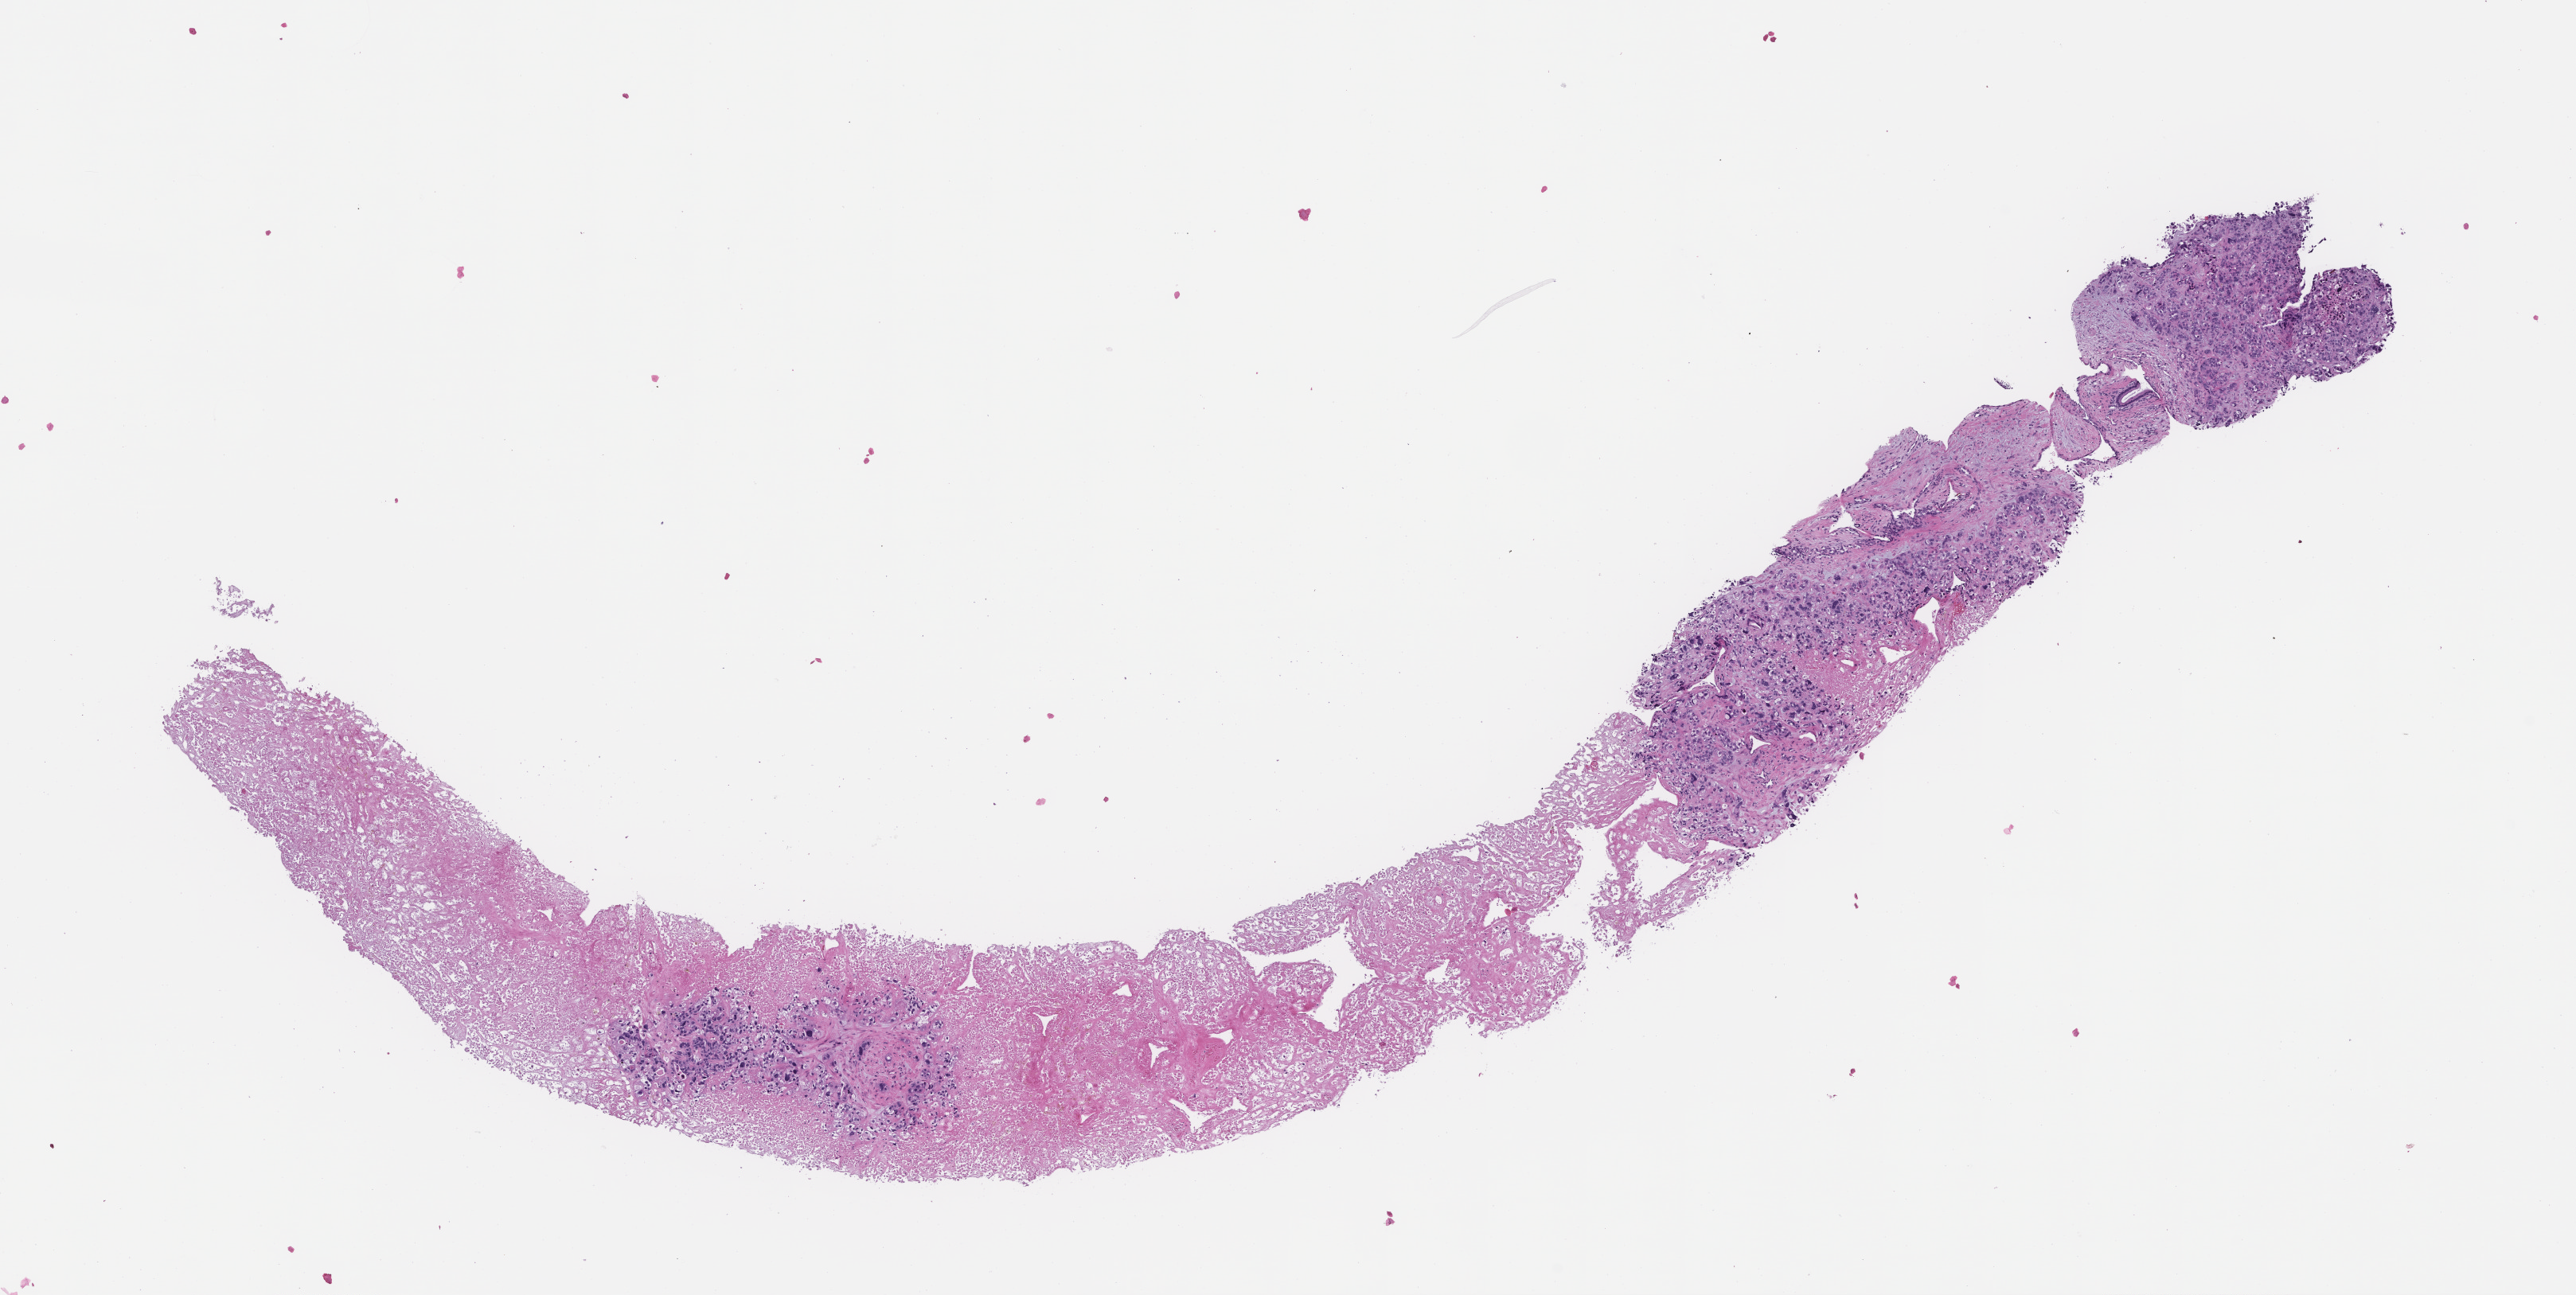
Digitized haematoxylin and eosin-stained section, low-resolution overview of the scanned area, about 13.1 x 6.6 mm. Formalin-fixed, paraffin-embedded (FFPE) tissue. Specimen time point: collected at disease progression. Patient: female.
- this section: metastatic tumor tissue
- primary diagnosis of the patient: Invasive Breast Carcinoma